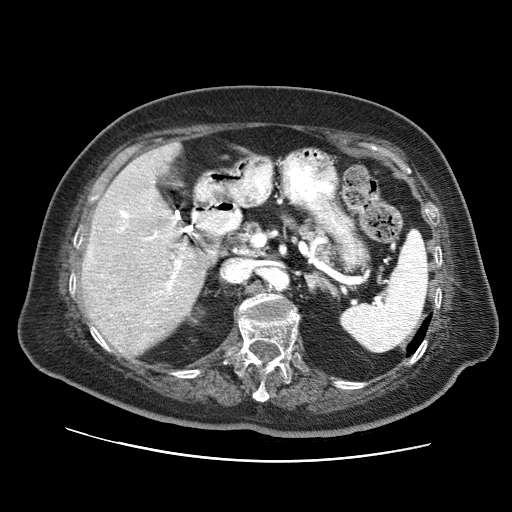
Contrast-enhanced abdominal CT (liver protocol), one axial slice; slice 36 of 73 in the series (ordered by position); soft-tissue window (W 400 / L 40 HU); 2.5 mm slice thickness; 512 × 512 image matrix. Case-level facts recorded for this patient, not image findings: diagnosis: hepatocellular carcinoma (patient treated with transarterial chemoembolisation; whether this scan precedes or follows treatment is not stated here); TNM stage (as recorded): Stage-I; Child-Pugh class: A; tumour differentiation: well differentiated.
Outlined on this slice (semi-automatically segmented with operator editing):
- liver parenchyma outside the tumour (the mass and vessels are separate outlines, so this box may not span the whole liver): bounding box [x1, y1, x2, y2] px = [82, 142, 216, 352]
- liver vessels: [88, 206, 214, 323]